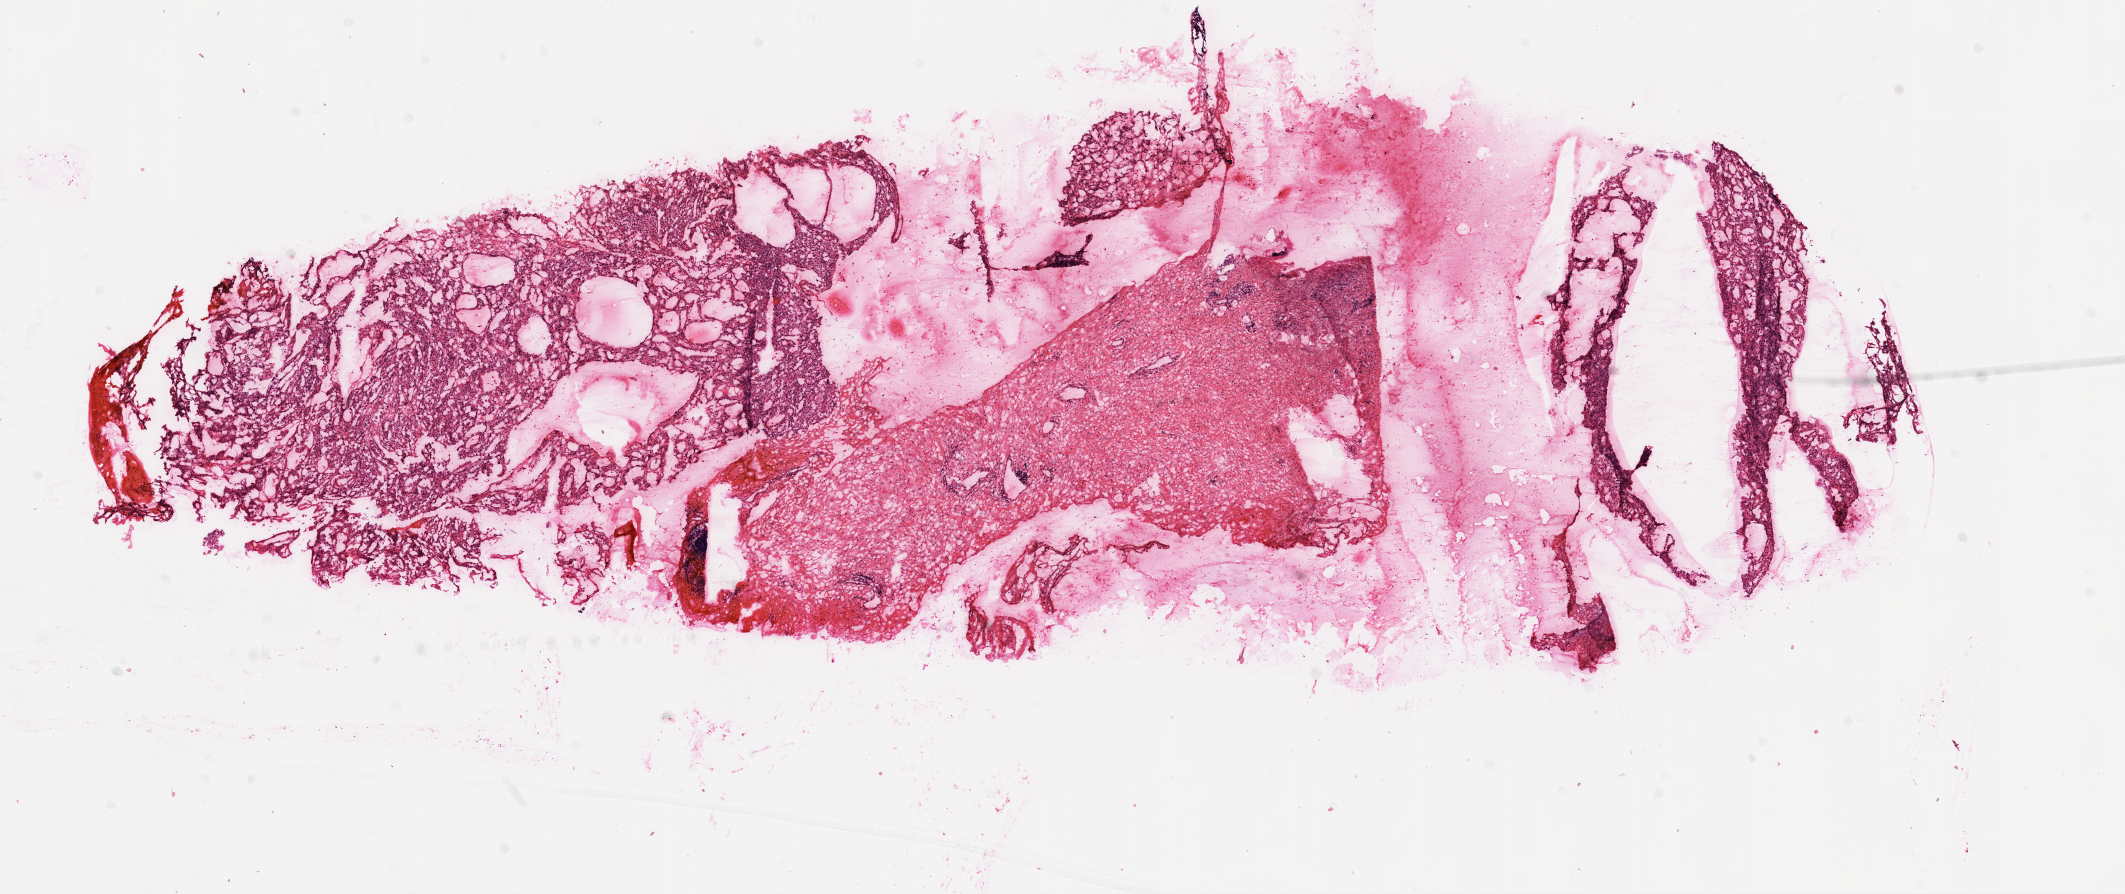
Digitized Hematoxylin and eosin (H&E) stained tissue section (whole slide) — whole scanned area (about 17.1 x 7.2 mm) shown as a low-resolution overview. Frozen section. Primary tumour sample from the kidney. Patient: female, age at initial diagnosis 63 years. Histologic grade: G4 (undifferentiated). Composition of this section per pathologist review: tumour cells 50%, tumour nuclei 80%, normal cells 0%, stromal cells 50%, necrosis 0%.
• TNM: T1a NX M0
• AJCC pathologic stage: I
• histologic diagnosis: Clear cell adenocarcinoma, NOS
• laterality: left